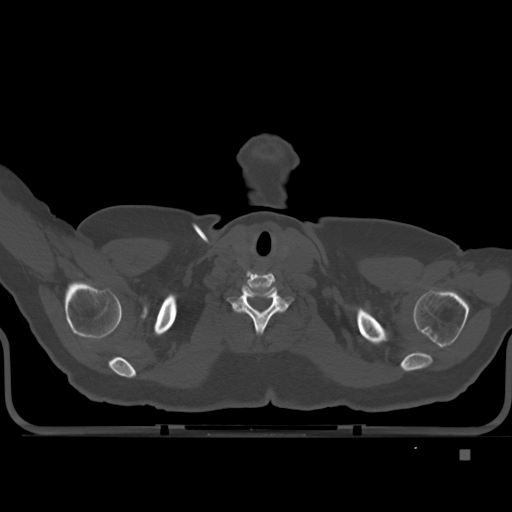
CT including the spine, one axial slice. Slice 412 of 477 in the series (ordered by position). Bone window (W 1800 / L 400 HU). 1.5 mm slice thickness. 512 × 512 image matrix, field of view 422 × 422 mm. Female patient, age 74 years. From the clinical record (not read from this slice): primary cancer: colon.
Annotated regions visible in this slice (semi-automatic segmentation, software-assisted and operator-edited):
- T1 vertebra: bounding box [x1, y1, x2, y2] px = [255, 311, 276, 332]